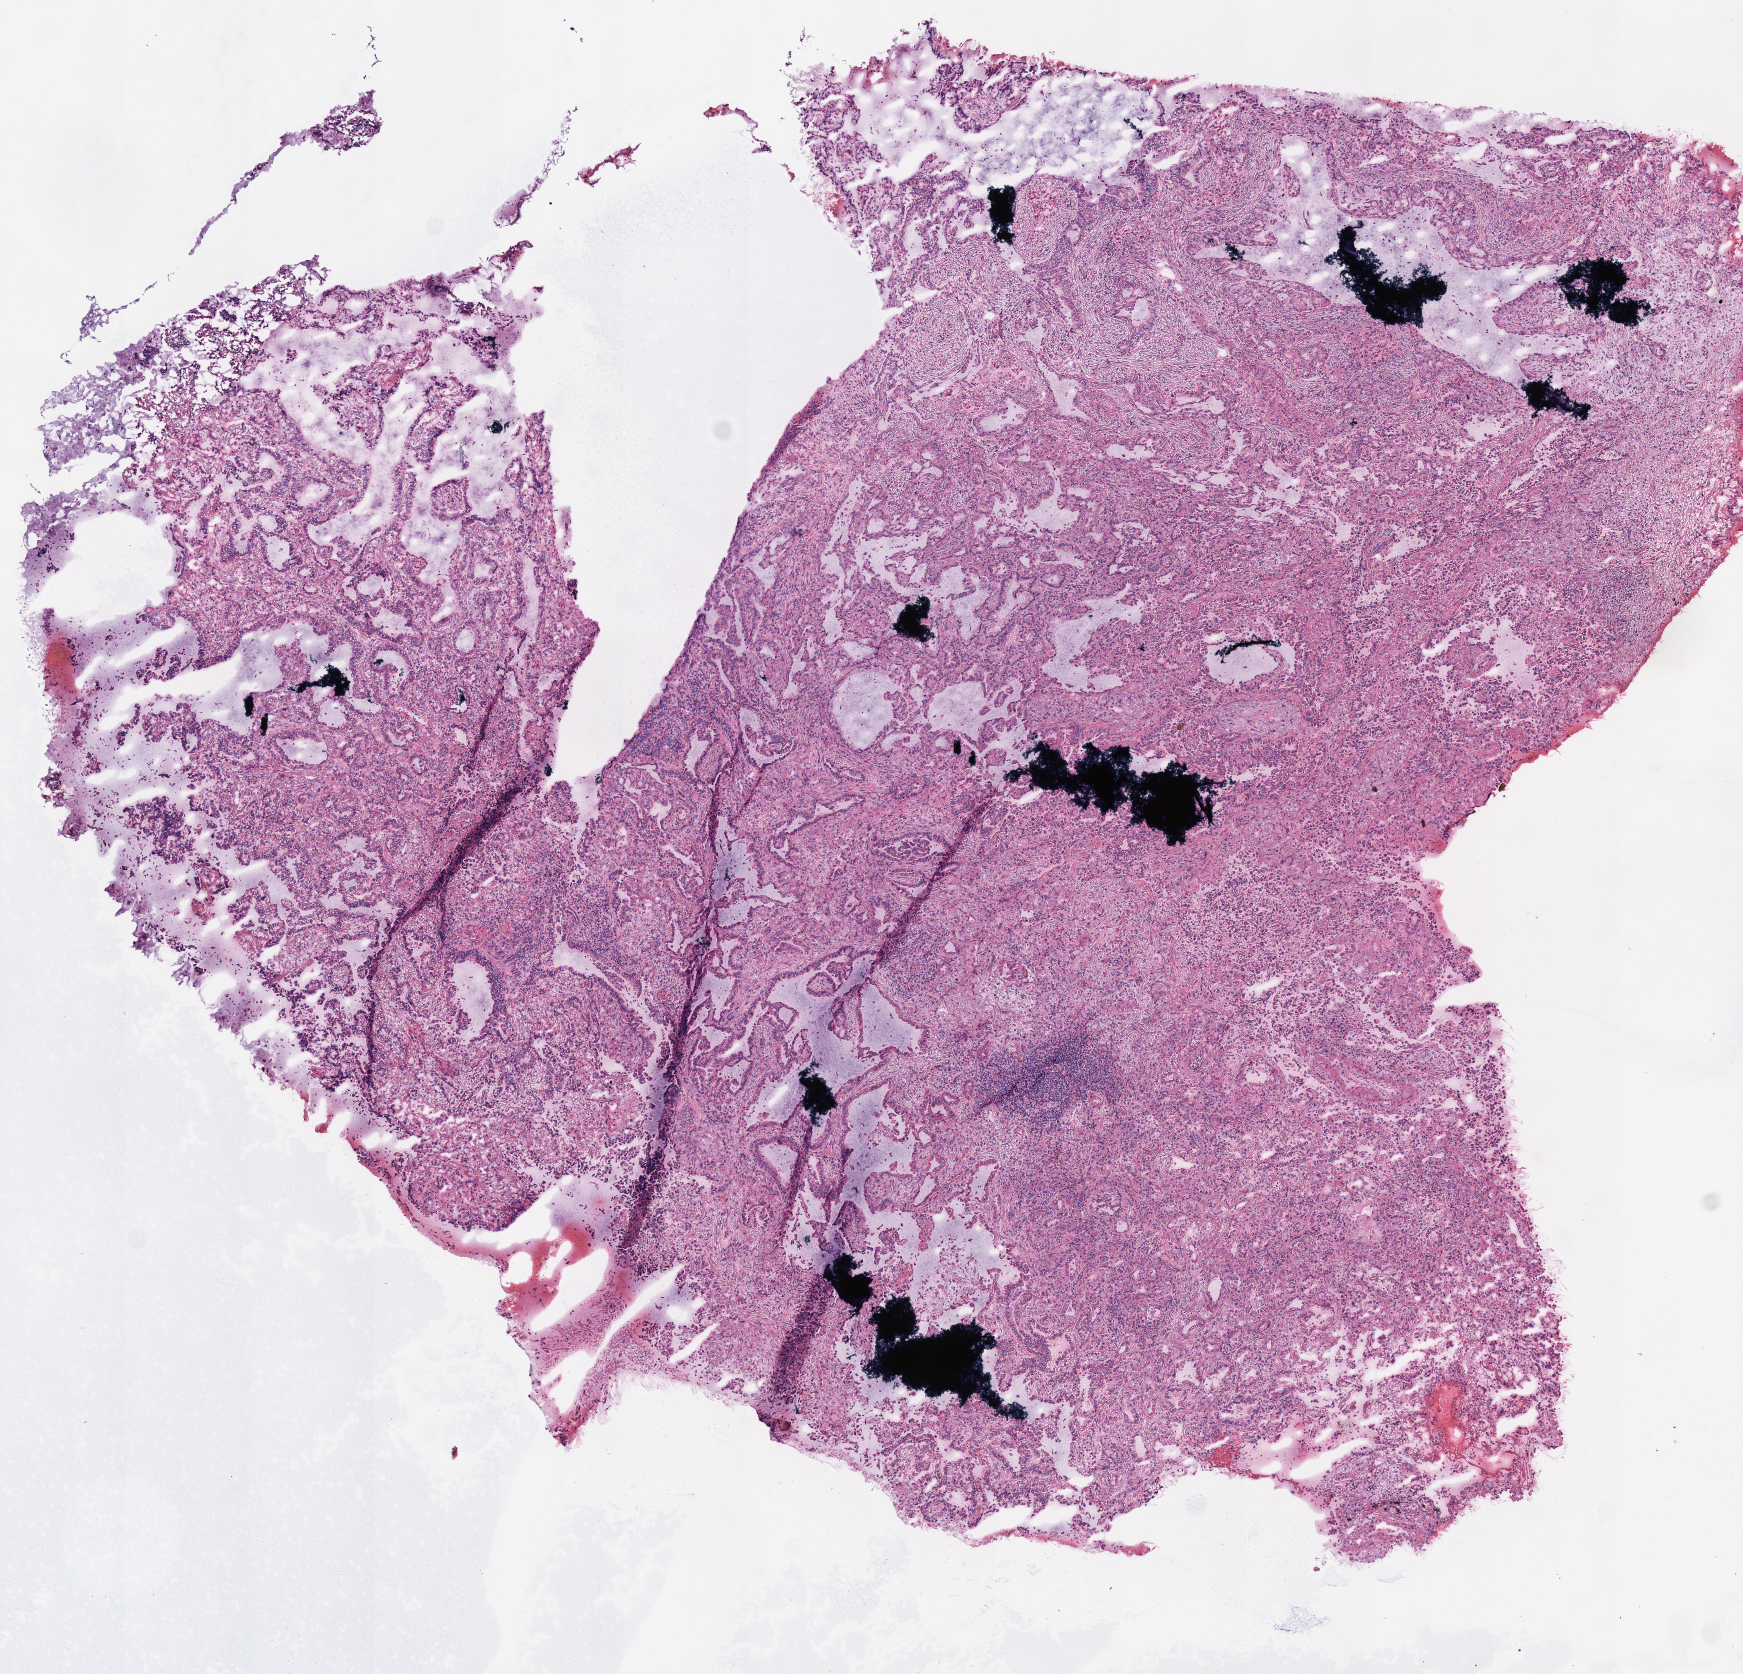
Digitized Hematoxylin and eosin (H&E) stained tissue section (whole slide) — low-resolution overview of the scanned area, about 6.9 x 6.6 mm (from a 40x scan); frozen section; lung, primary tumour sample. Patient: female, age at initial diagnosis 65 years. Composition of this section per pathologist review: tumour cells 100%, tumour nuclei 85%, normal cells 0%, stromal cells 0%, necrosis 0%. Infiltration values recorded for this section: lymphocyte infiltration 5%.
Laterality: left. AJCC pathologic stage: IIA. Histologic diagnosis: Adenocarcinoma, NOS (upper lobe, lung).